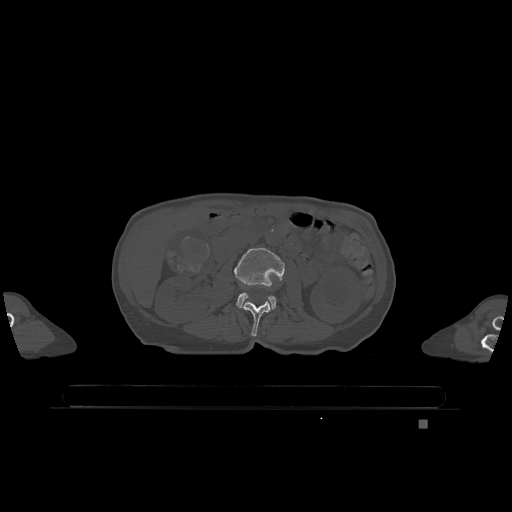
CT including the spine, one axial slice; position 389 of 1317 along the scan axis; bone window (W 1800 / L 400 HU); 0.5 mm slice thickness; 512 × 512 image matrix. Patient: female, 74 years. Case-level facts recorded for this patient, not image findings: primary cancer: lung.
Annotated regions visible in this slice (semi-automatically segmented with operator editing):
- L2 vertebra: box from (x=243, y=301) to (x=270, y=337) px
- L3 vertebra: (x=234, y=248)–(x=285, y=310)